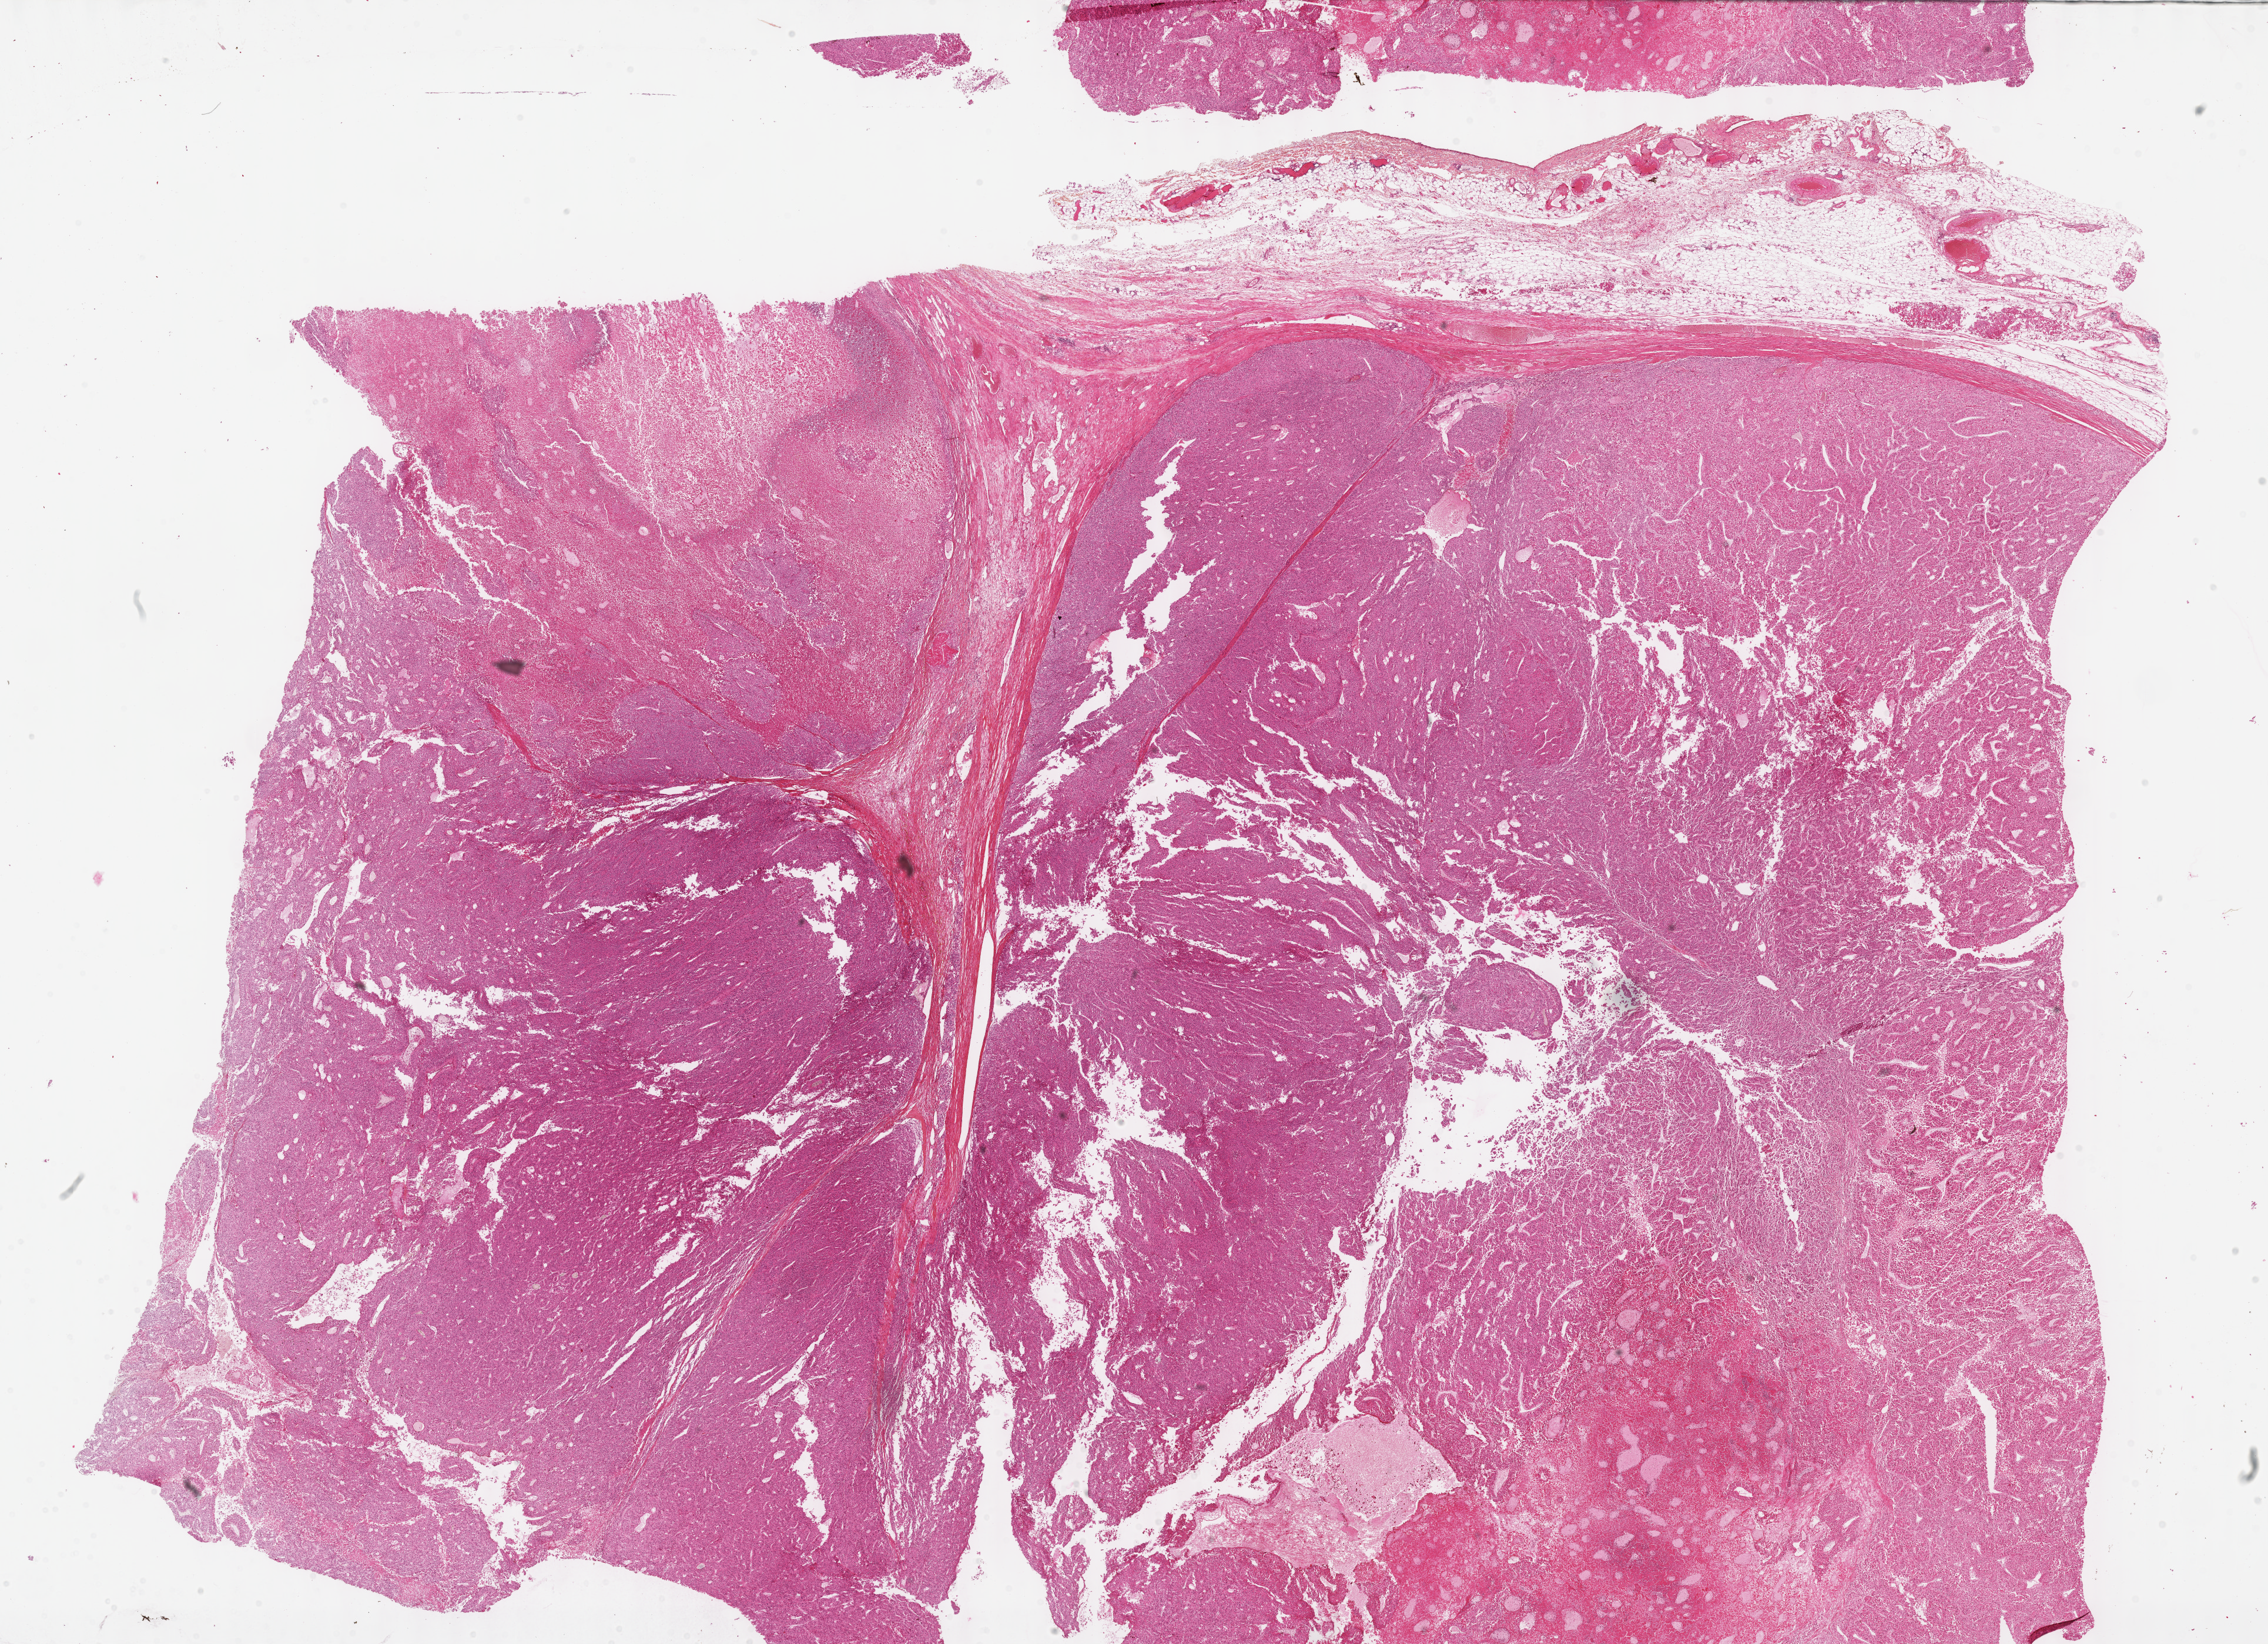
Hematoxylin and eosin (H&E) stained whole-slide image, low-resolution overview of the scanned area, about 31.2 x 22.6 mm (slide scanned at 40x); formalin-fixed paraffin-embedded (FFPE) diagnostic section; adrenal cortex, primary tumour sample. Female patient; age at initial diagnosis 61 years.
Laterality: right. Pathologic diagnosis: Adrenal cortical carcinoma. Lymph nodes positive (case pathology): 0 of 19 examined.